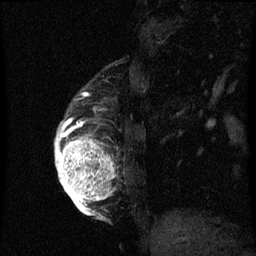
Breast MRI (dynamic contrast-enhanced), one sagittal slice; dynamic contrast-enhanced series, image 2 of 3 at this slice position (ordered by acquisition); 1.5 T; TE 4.2 ms, TR 8 ms; 2 mm slice thickness; 256 × 256 image matrix, field of view 180 × 180 mm. Female patient, age 56 years.
Outlined on this slice (semi-automatic segmentation, software-assisted and operator-edited):
- analysis volume of interest (the breast-tissue region the enhancement analysis was run in; not a lesion): bounding box (x1, y1, x2, y2) in pixels: (56, 96, 119, 219)
- tumour enhancement mask (voxels above the 70 % enhancement threshold inside the analysis volume of interest): (56, 122, 115, 219)